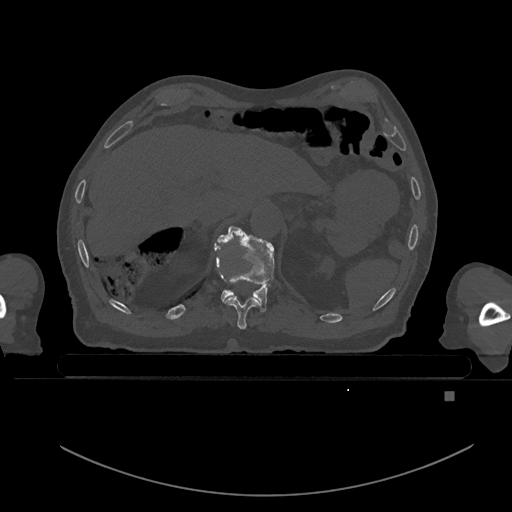
CT including the spine, one axial slice. Position 58 of 969 along the scan axis. Bone window (W 1800 / L 400 HU). 0.5 mm slice thickness. 512 × 512 image matrix. Patient: male, 82 years. Case-level facts recorded for this patient, not image findings: primary cancer: prostate; vertebrae with lytic lesions (as recorded): T11, T9, T8, T2.
Structures marked on this image (semi-automatically segmented with operator editing):
- T10 vertebra: box from (x=215, y=242) to (x=260, y=330) px
- T11 vertebra: (x=218, y=225)–(x=275, y=312)